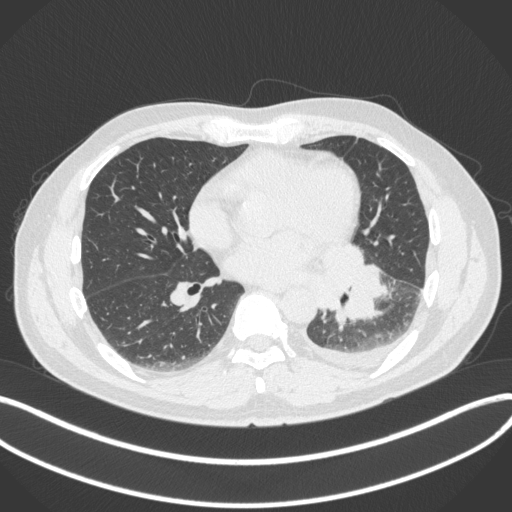
Chest CT, one axial slice. Reconstruction kernel B31f. 120 kVp. Lung window (W 1500 / L -600 HU). 512 × 512 image matrix. Male patient, age 58 years. From the clinical record (not read from this slice): clinical TNM (as recorded): T3 N1 M1b.
Annotated regions visible in this slice (bounding box drawn by a radiologist):
- lung tumour (recorded histology: small cell carcinoma): bounding box (x1, y1, x2, y2) in pixels: (312, 244, 384, 329)